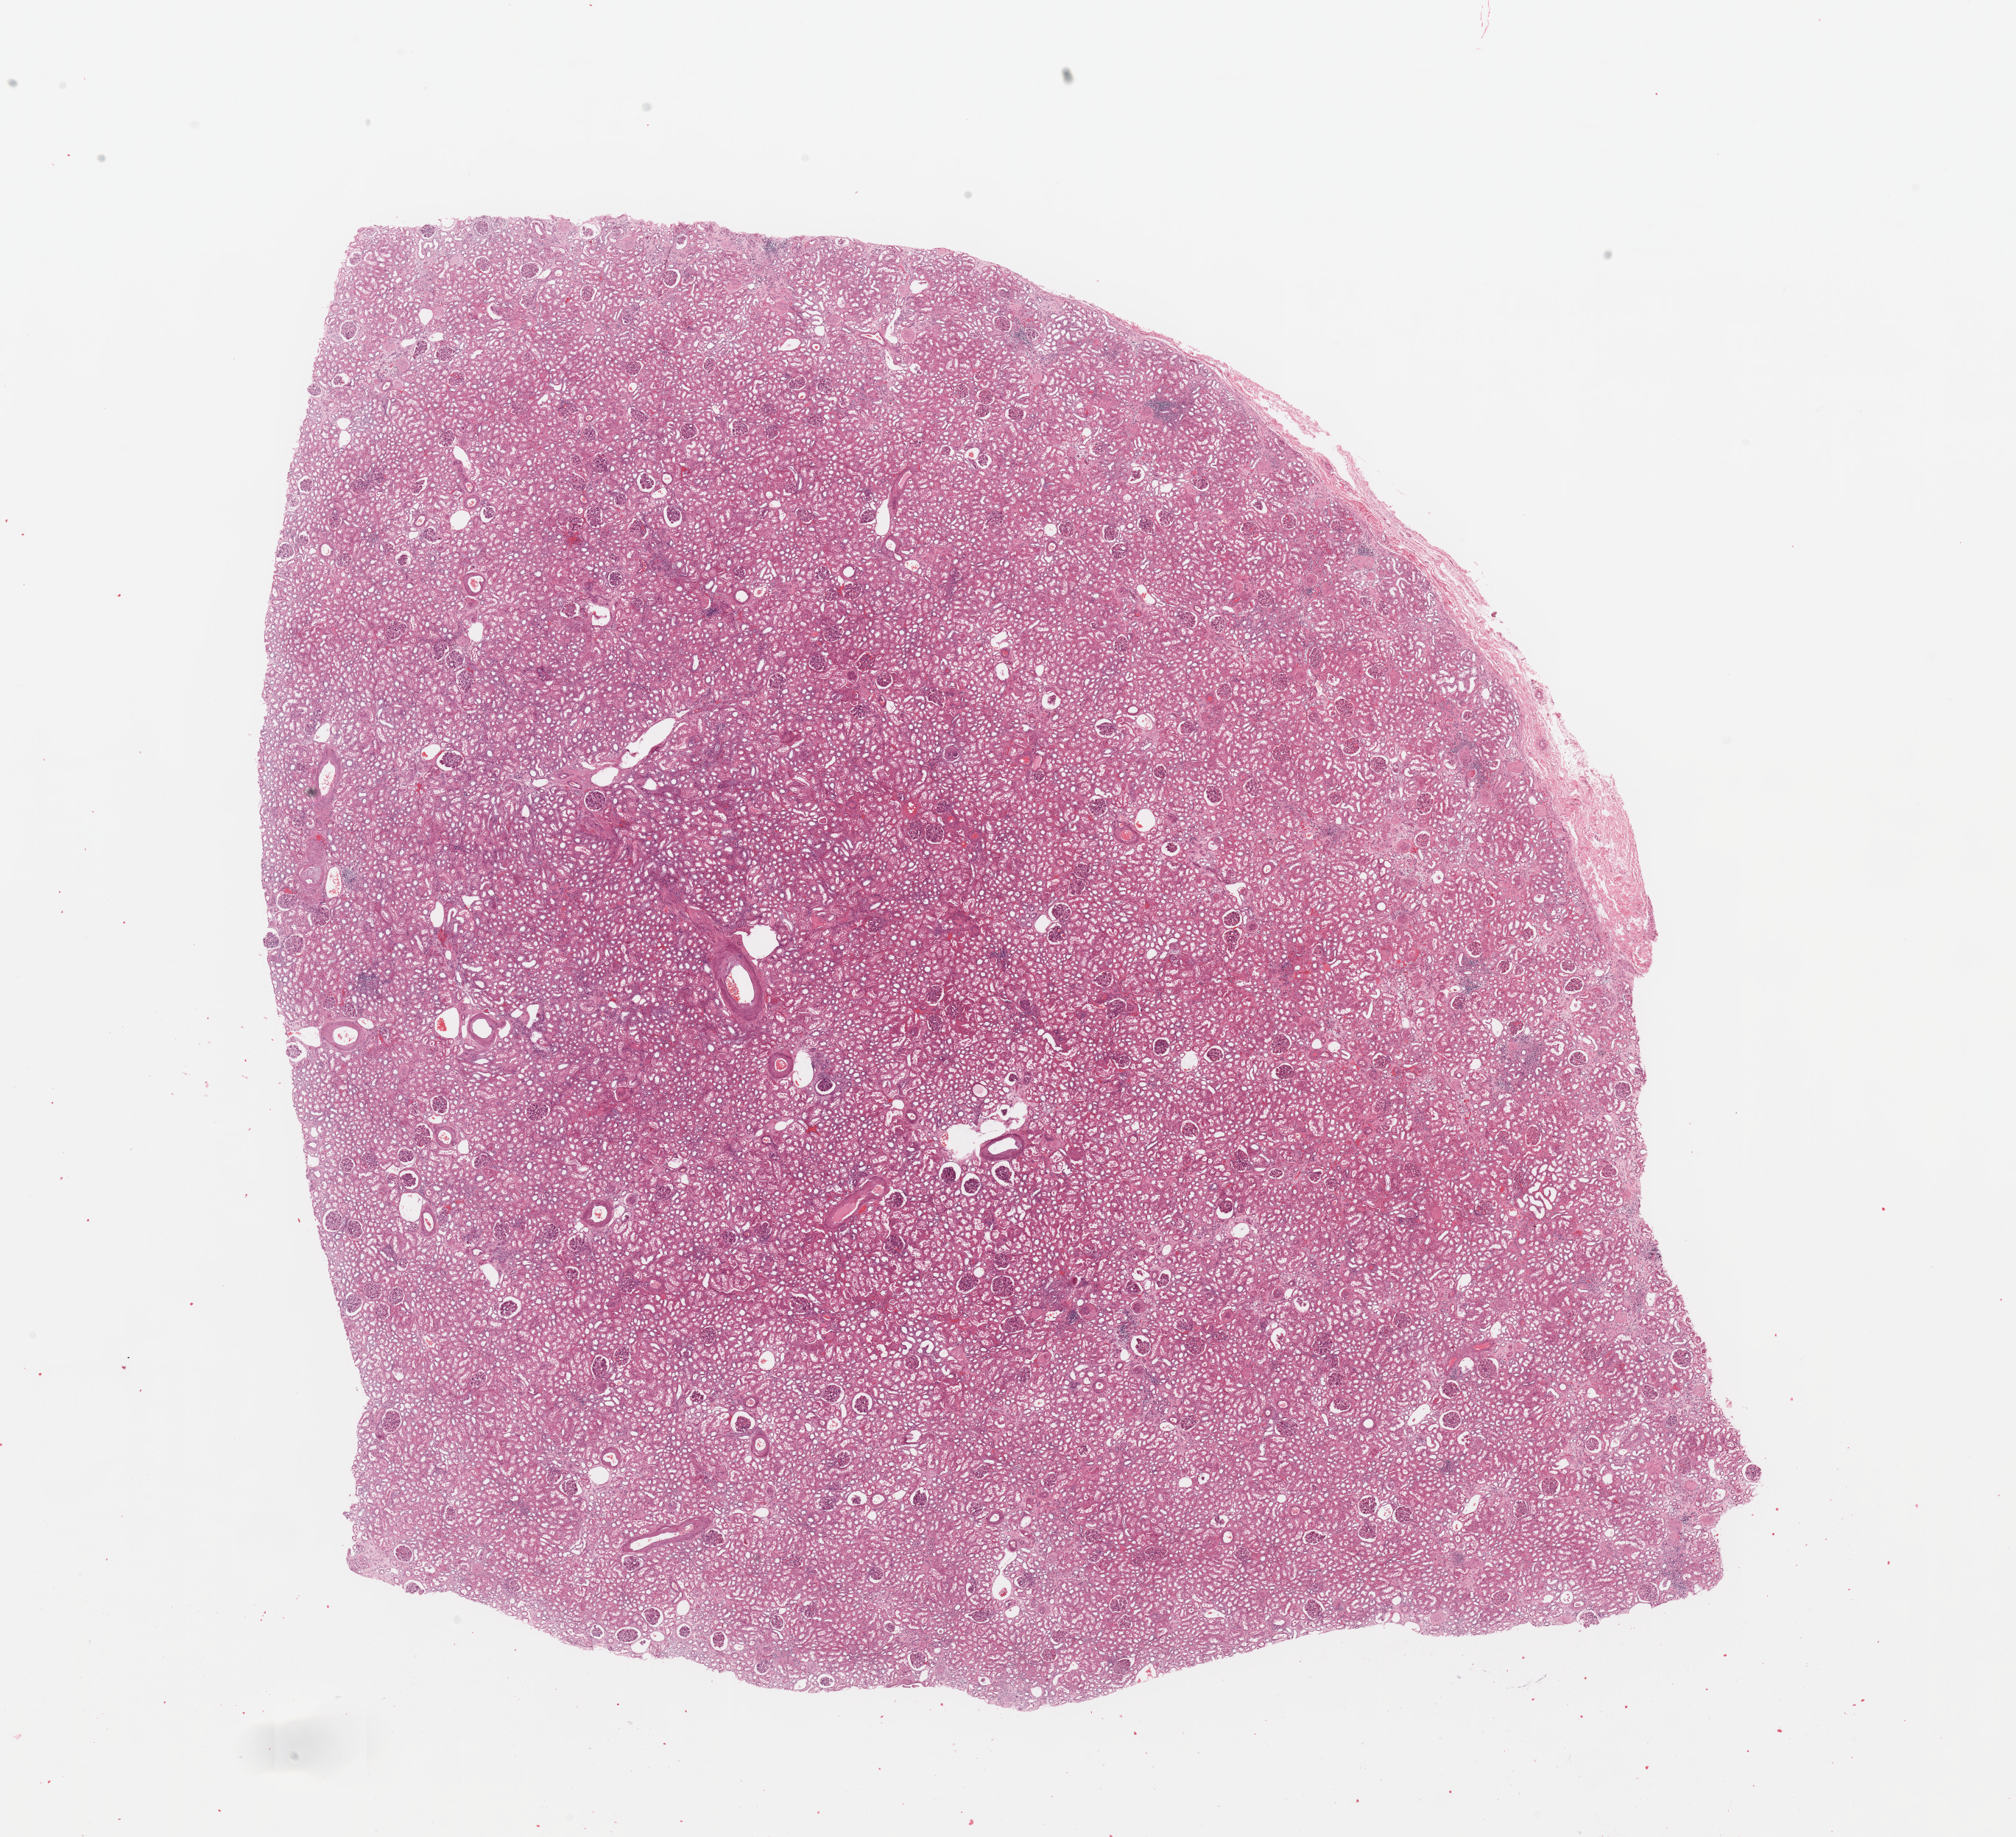
Digitized H&E-stained tissue section (whole slide) — a low-resolution overview of the entire scanned area, about 21.7 x 19.7 mm; kidney, normal (non-tumour) tissue. 76-year-old female patient.
- this section: normal (non-tumour) tissue from the same patient
- patient diagnosis: Renal cell carcinoma, NOS